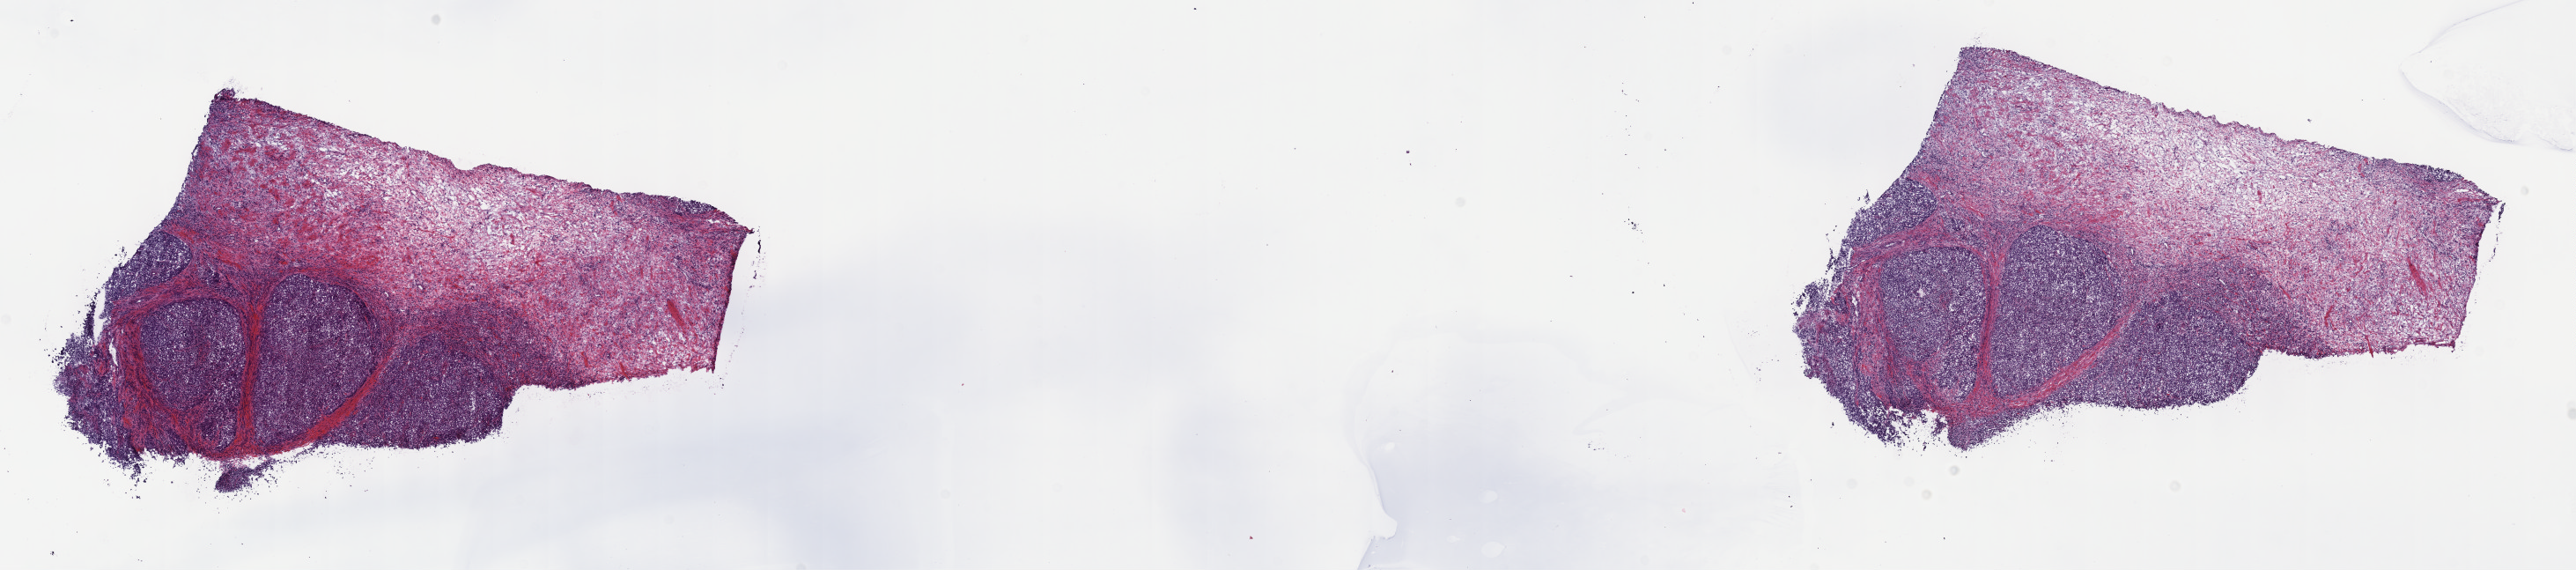
Whole-slide histology image, H&E — whole scanned area (about 23.7 x 5.2 mm, from a 40x scan) shown as a low-resolution overview, frozen section from the top of the tissue portion, primary tumour sample from the thymus. Patient: male, age at initial diagnosis 44 years. Composition of this section per pathologist review: tumour cells 42%, tumour nuclei 70%, normal cells 0%, stromal cells 55%, necrosis 3%. Infiltration values recorded for this section: lymphocyte infiltration 25%, monocyte infiltration 2%, neutrophil infiltration 2%.
* pathologic diagnosis: Thymic carcinoma, NOS (anterior mediastinum)